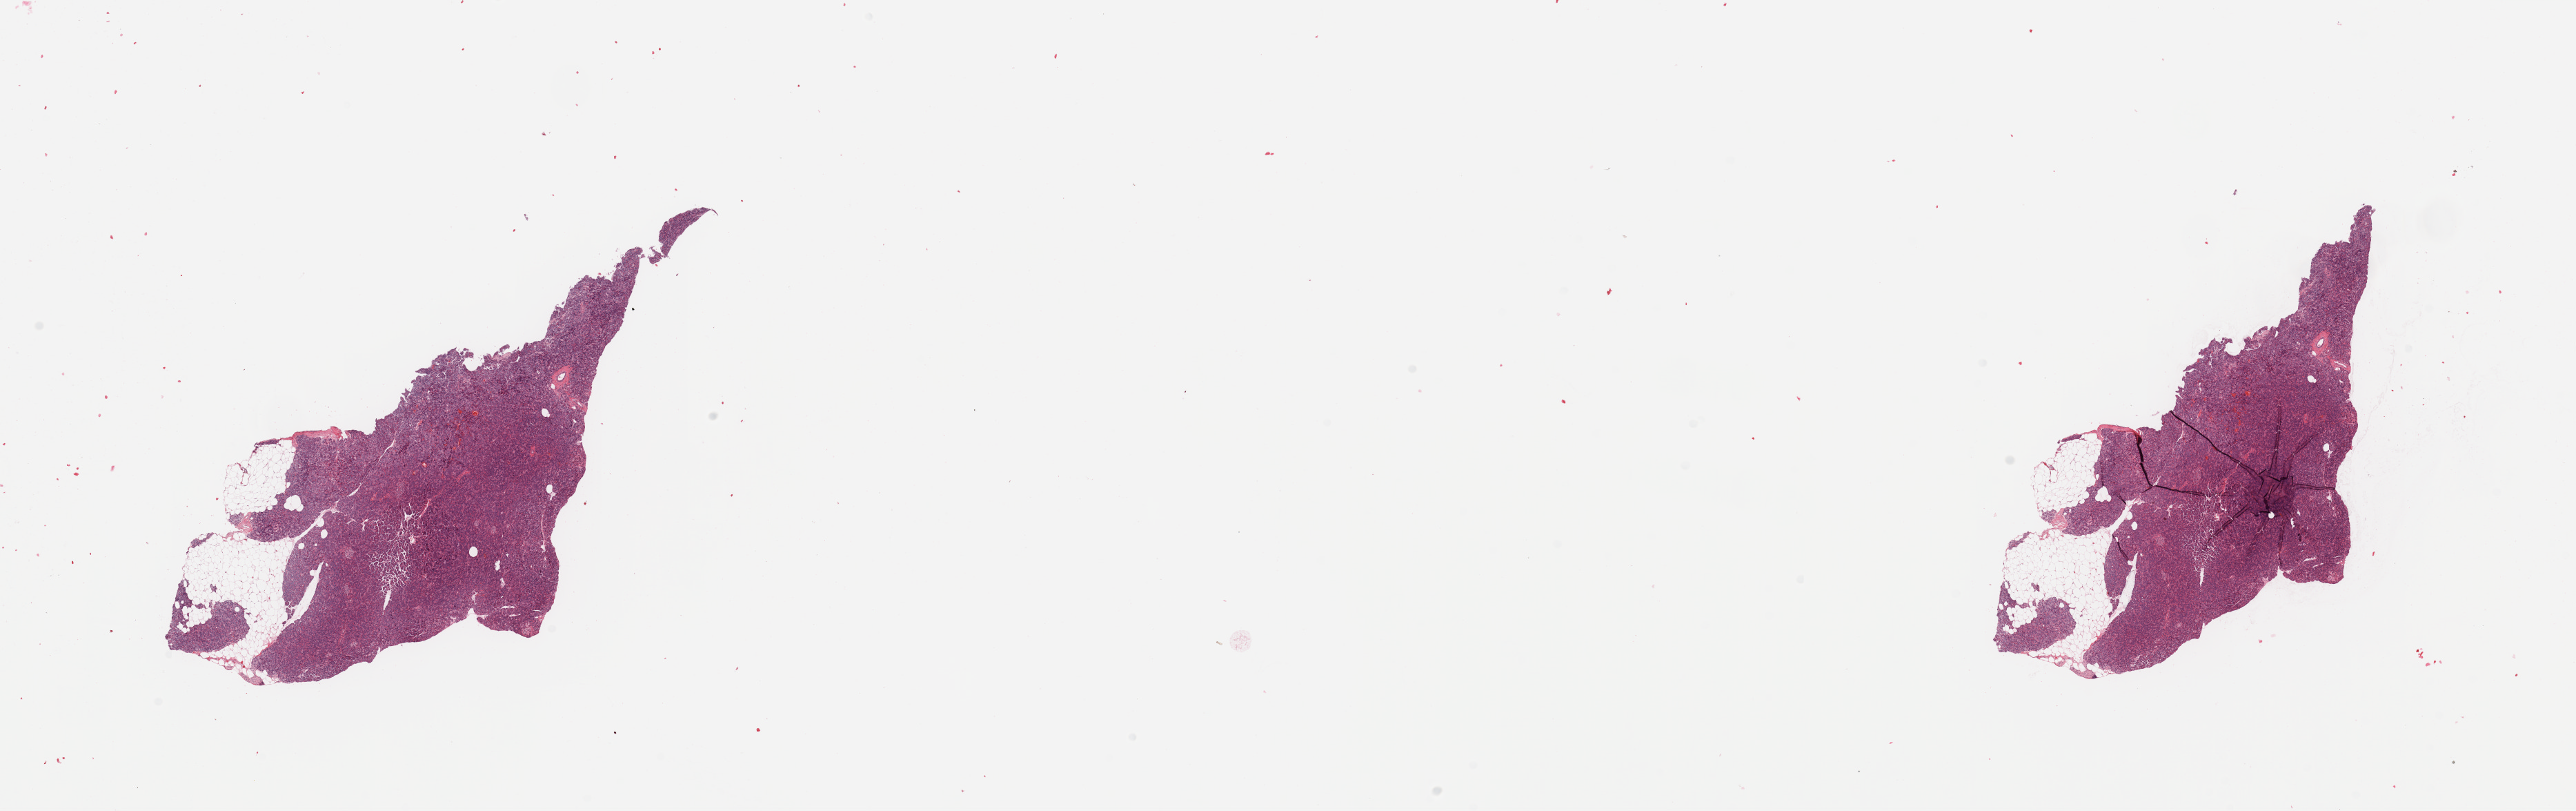
H&E whole-slide image — a low-resolution overview of the entire scanned area, about 29.5 x 9.3 mm (acquisition: 20x scan). Normal (non-tumour) tissue sample, sampled site: pancreas. Patient: male, age 74 years.
This section: normal (non-tumour) tissue from the same patient. Patient diagnosis: Infiltrating duct carcinoma, NOS.